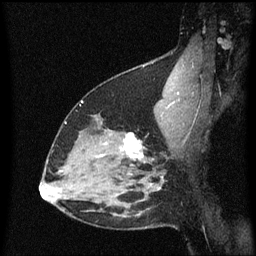
Breast MRI (dynamic contrast-enhanced), one sagittal slice. Slice 43 of 60 in the series (ordered by position). Dynamic contrast-enhanced series, image 2 of 3 at this slice position (ordered by acquisition). 1.5 T. TE 4.2 ms, TR 8.4 ms. 2 mm slice thickness. 256 × 256 image matrix, field of view 200 × 200 mm. Patient: female, 38 years. From the clinical record (not read from this slice): setting: breast cancer imaged before/during neoadjuvant chemotherapy; receptor status: HR-positive, HER2-negative.
Outlined on this slice (semi-automatic segmentation, software-assisted and operator-edited):
- analysis volume of interest (the breast-tissue region the enhancement analysis was run in; not a lesion): bounding box [x1, y1, x2, y2] px = [122, 132, 154, 163]
- tumour enhancement mask (voxels above the 70 % enhancement threshold inside the analysis volume of interest): [124, 132, 145, 159]